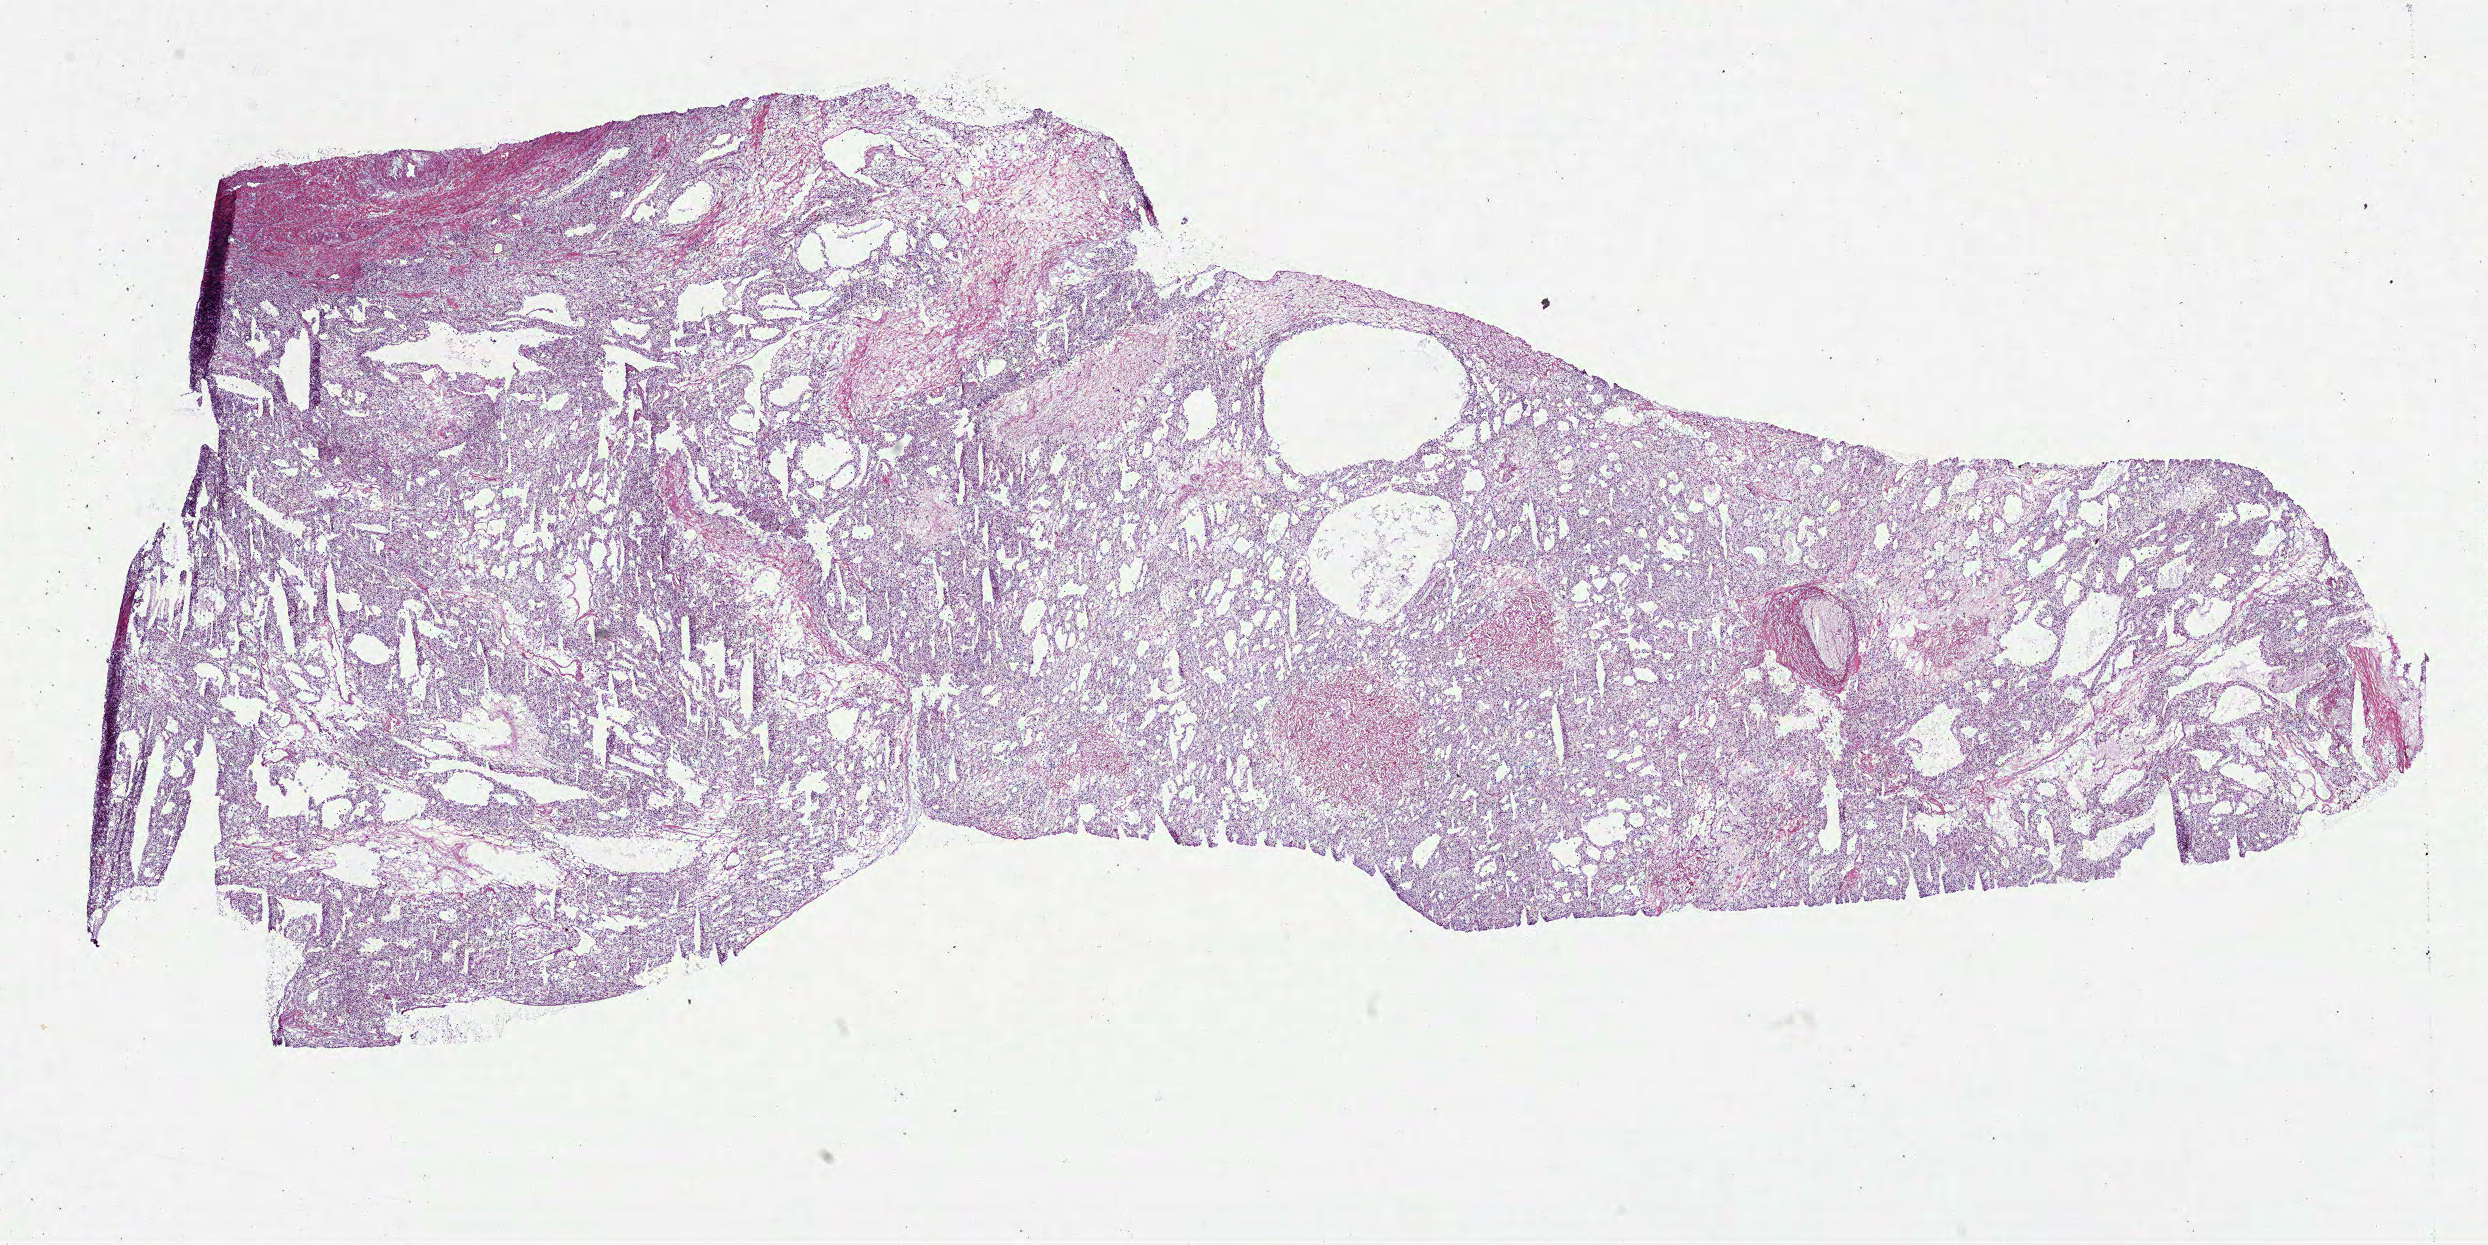
H&E-stained whole-slide image, shown as a low-resolution overview of the whole scanned area (about 20.1 x 10.0 mm, slide scanned at 40x); frozen section from the bottom of the tissue portion; kidney, primary tumour sample. Female patient; age at initial diagnosis 67 years. Histologic grade: G3 (poorly differentiated). Slide review estimates, as recorded: tumour cells 88%, tumour nuclei 85%, normal cells 0%, stromal cells 12%, necrosis 0%.
Diagnosis: Clear cell adenocarcinoma, NOS. AJCC pathologic stage: I (7th edition).